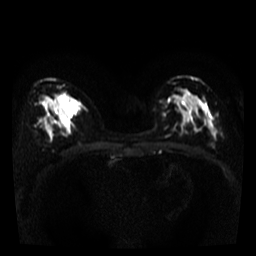
Breast MRI, one axial slice. Diffusion-weighted series; image 2 of 4 stored at this slice position (different b-values; order by instance number). 3 T. 5 mm slice thickness. 256 × 256 image matrix. Female patient.
Annotated regions visible in this slice (outlined manually by an expert reader):
- tumour on diffusion-weighted imaging: bounding box (x1, y1, x2, y2) in pixels: (60, 96, 78, 115)